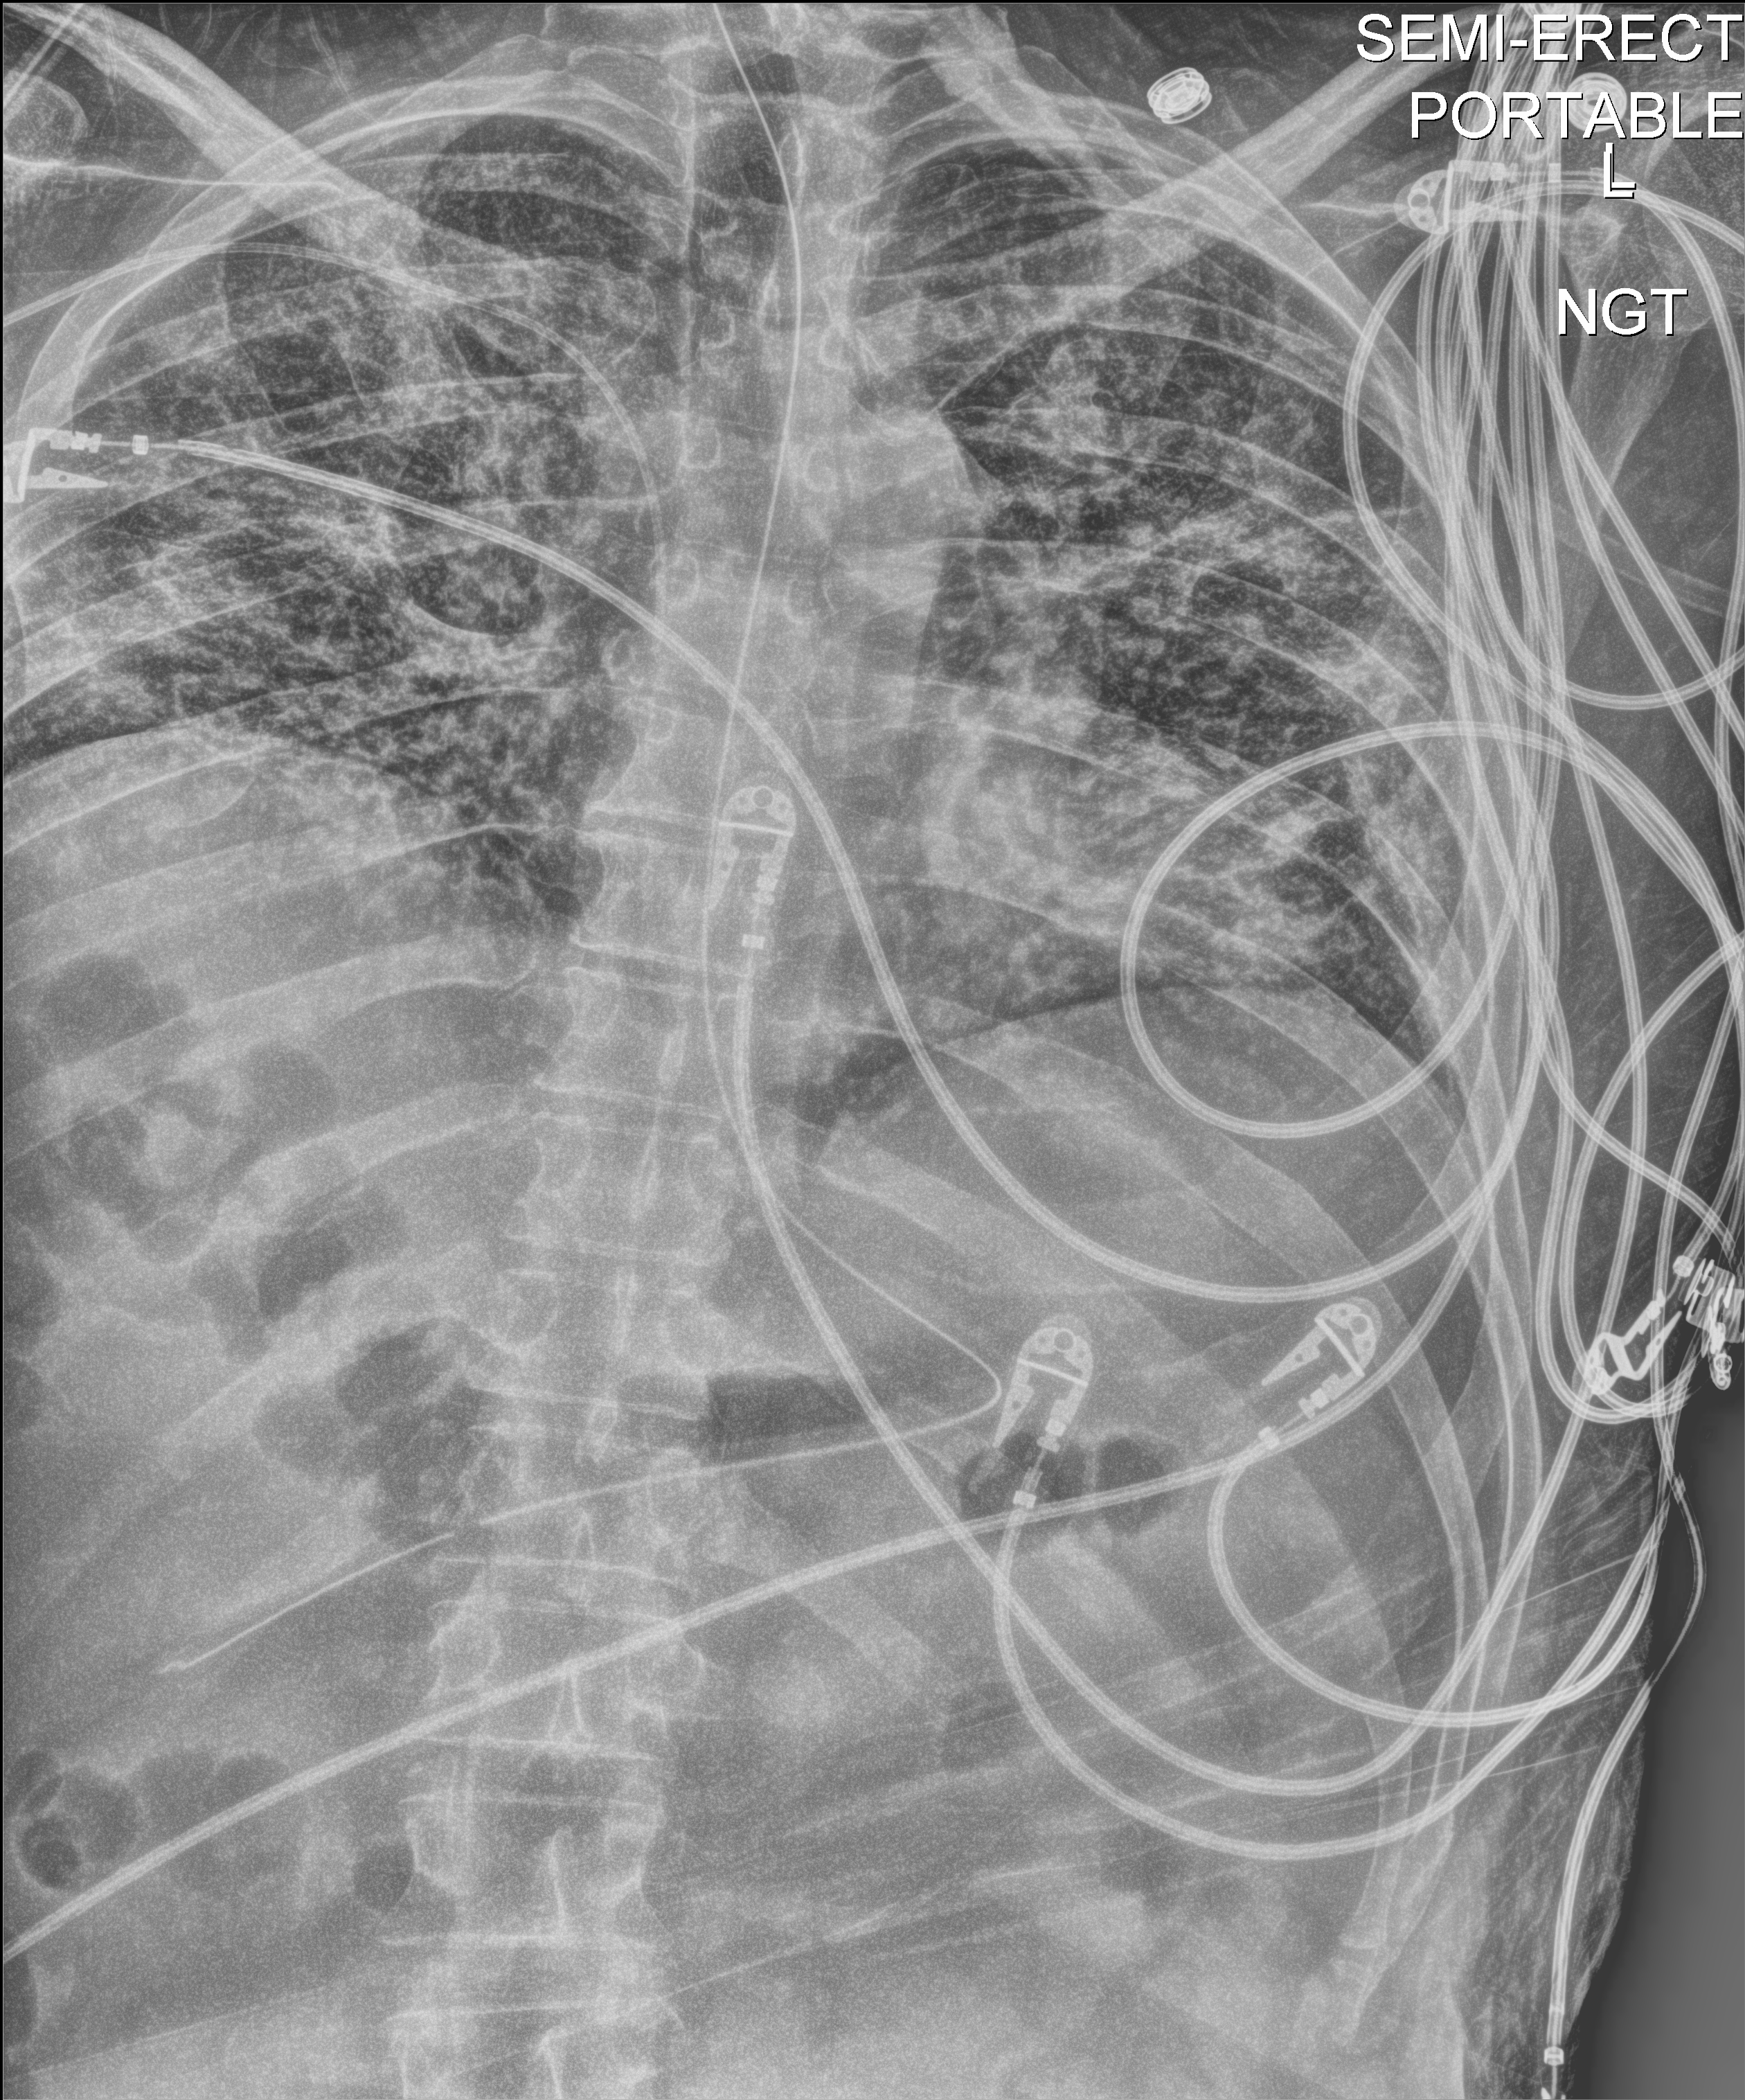
Portable chest radiograph; anteroposterior (AP) projection. Male patient hospitalised with COVID-19, age 18–59 years.
Admission-level facts for this patient (not findings on this image; timing relative to this image not recorded): admitted to intensive care during this hospital stay: yes; length of hospital stay: 48 days.